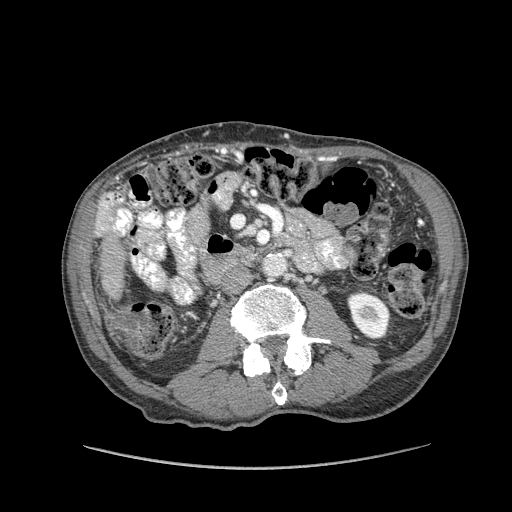
Contrast-enhanced abdominal CT (liver protocol), one axial slice; soft-tissue window (W 400 / L 40 HU); 2.5 mm slice thickness; 512 × 512 image matrix, field of view 400 × 400 mm. Case-level facts recorded for this patient, not image findings: diagnosis: hepatocellular carcinoma (patient treated with transarterial chemoembolisation; whether this scan precedes or follows treatment is not stated here); TNM stage (as recorded): Stage-IIIA; Child-Pugh class: A; tumour nodularity: multinodular; tumour size: 9.9 cm.
Outlined on this slice (semi-automatic segmentation, software-assisted and operator-edited):
- liver parenchyma outside the tumour (the mass and vessels are separate outlines, so this box may not span the whole liver): box from (x=94, y=192) to (x=124, y=300) px
- liver vessels: (x=100, y=194)–(x=121, y=230)